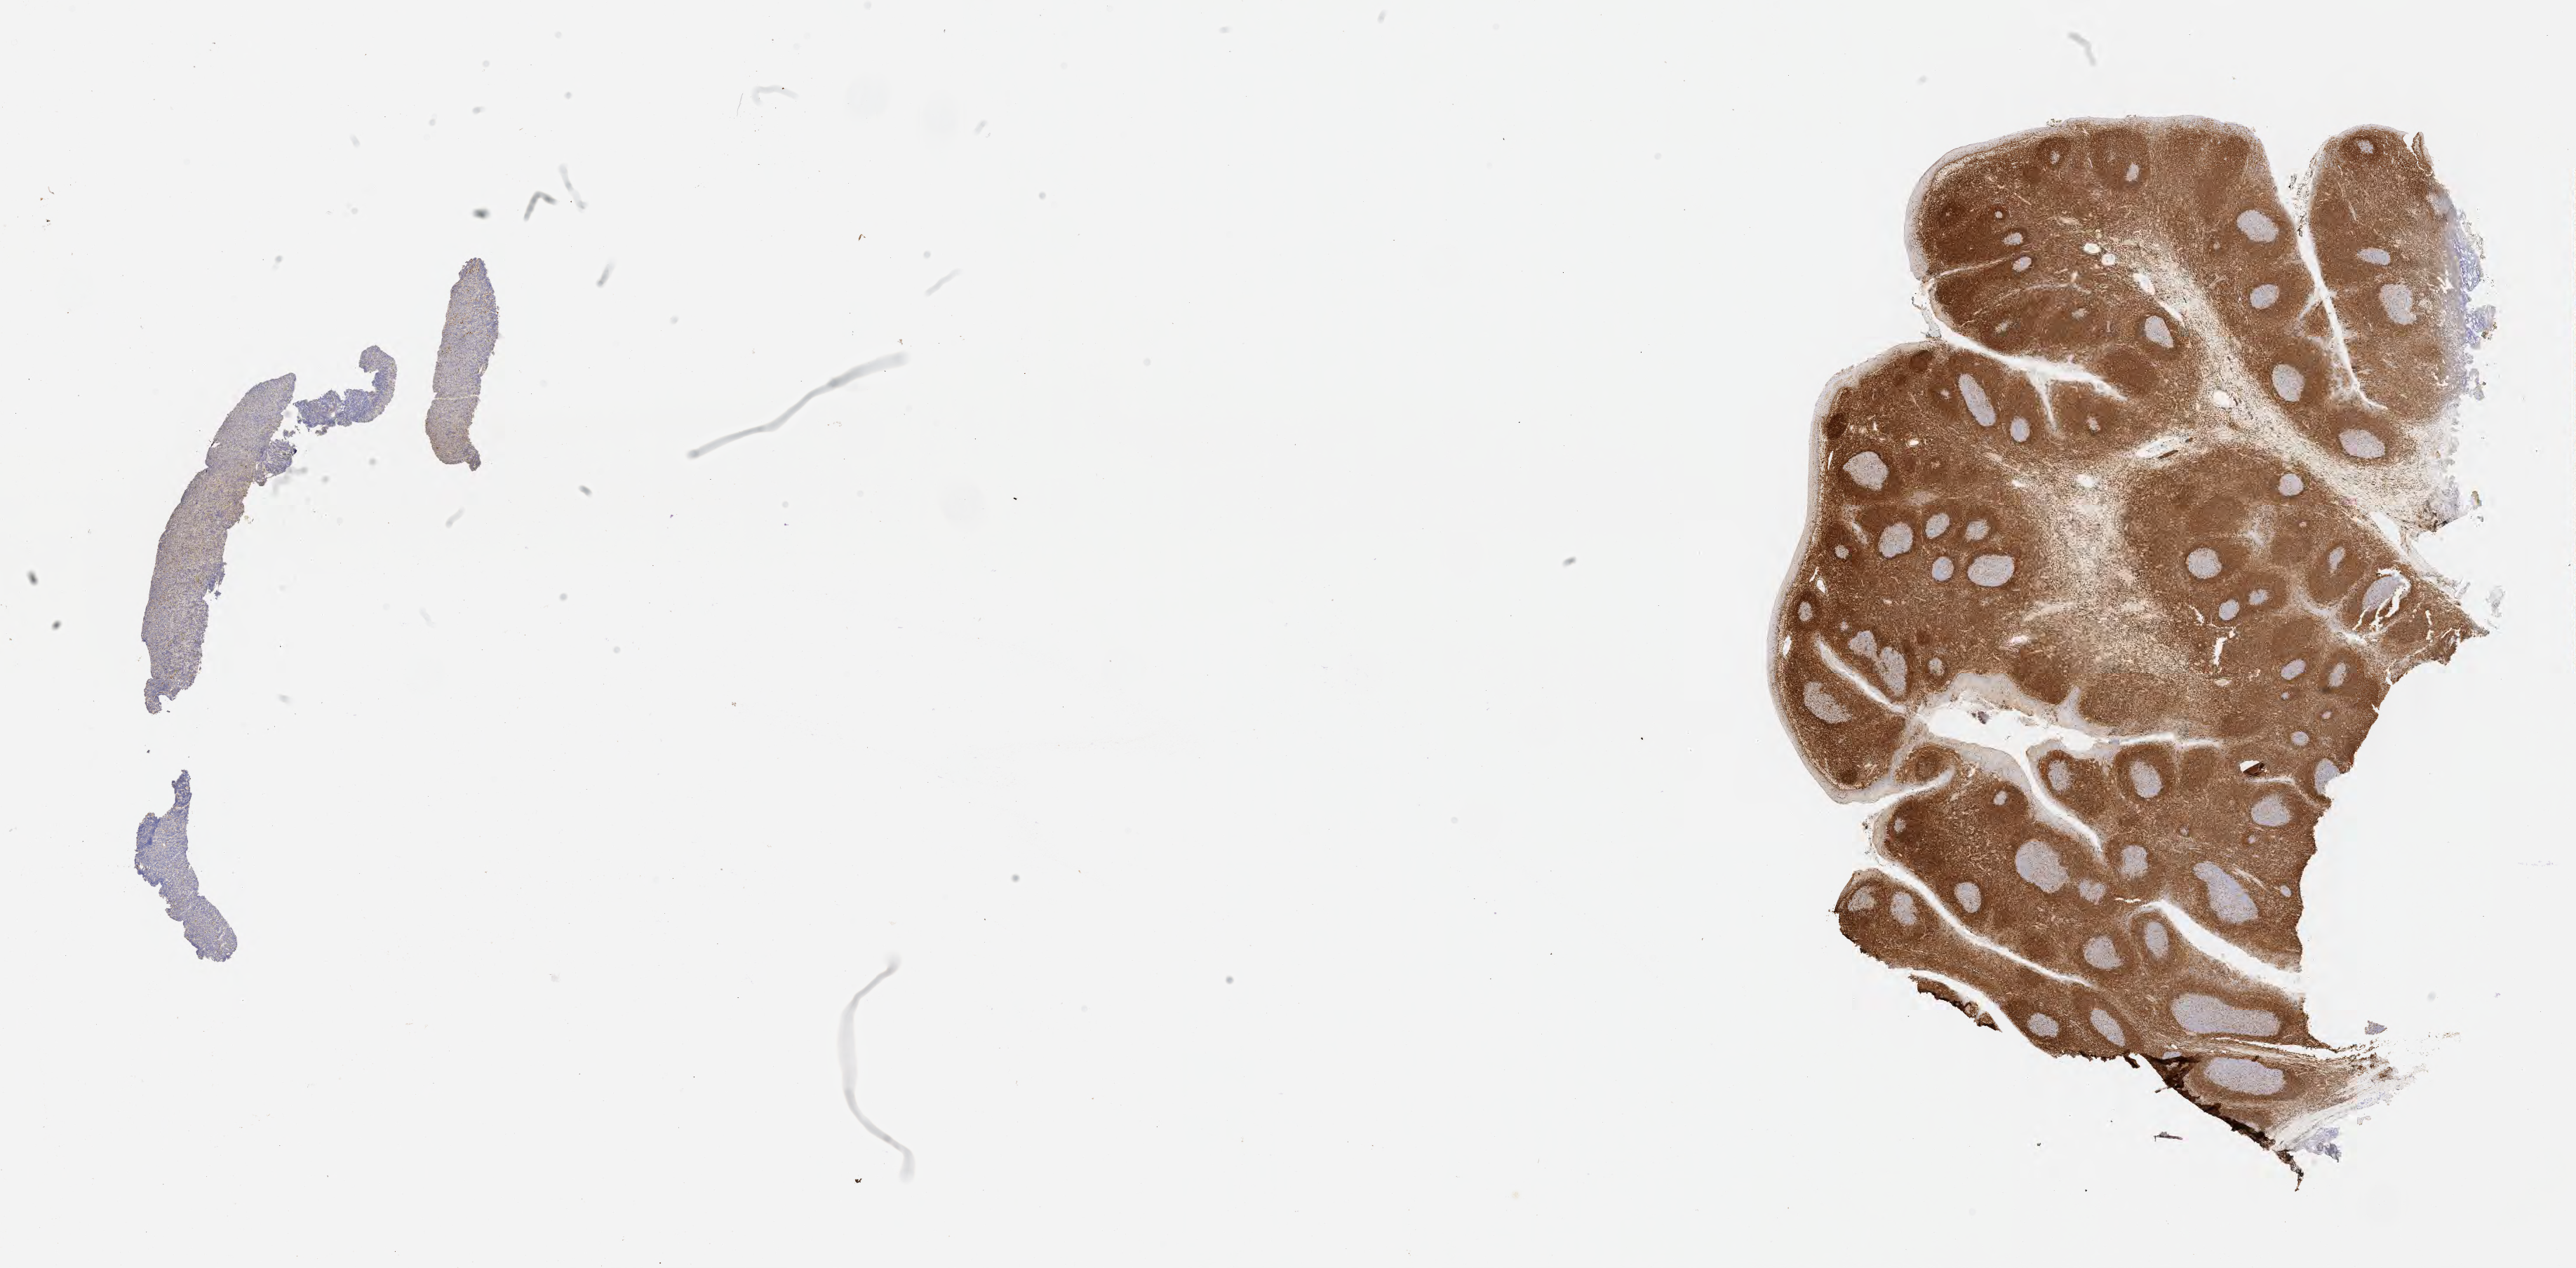
IHC for BCL2, whole-slide image — a low-resolution overview of the entire scanned area, about 29.7 x 14.6 mm; specimen: tumor tissue. Patient male; aged 10.
Diagnosis: Diffuse large B-cell lymphoma, NOS.